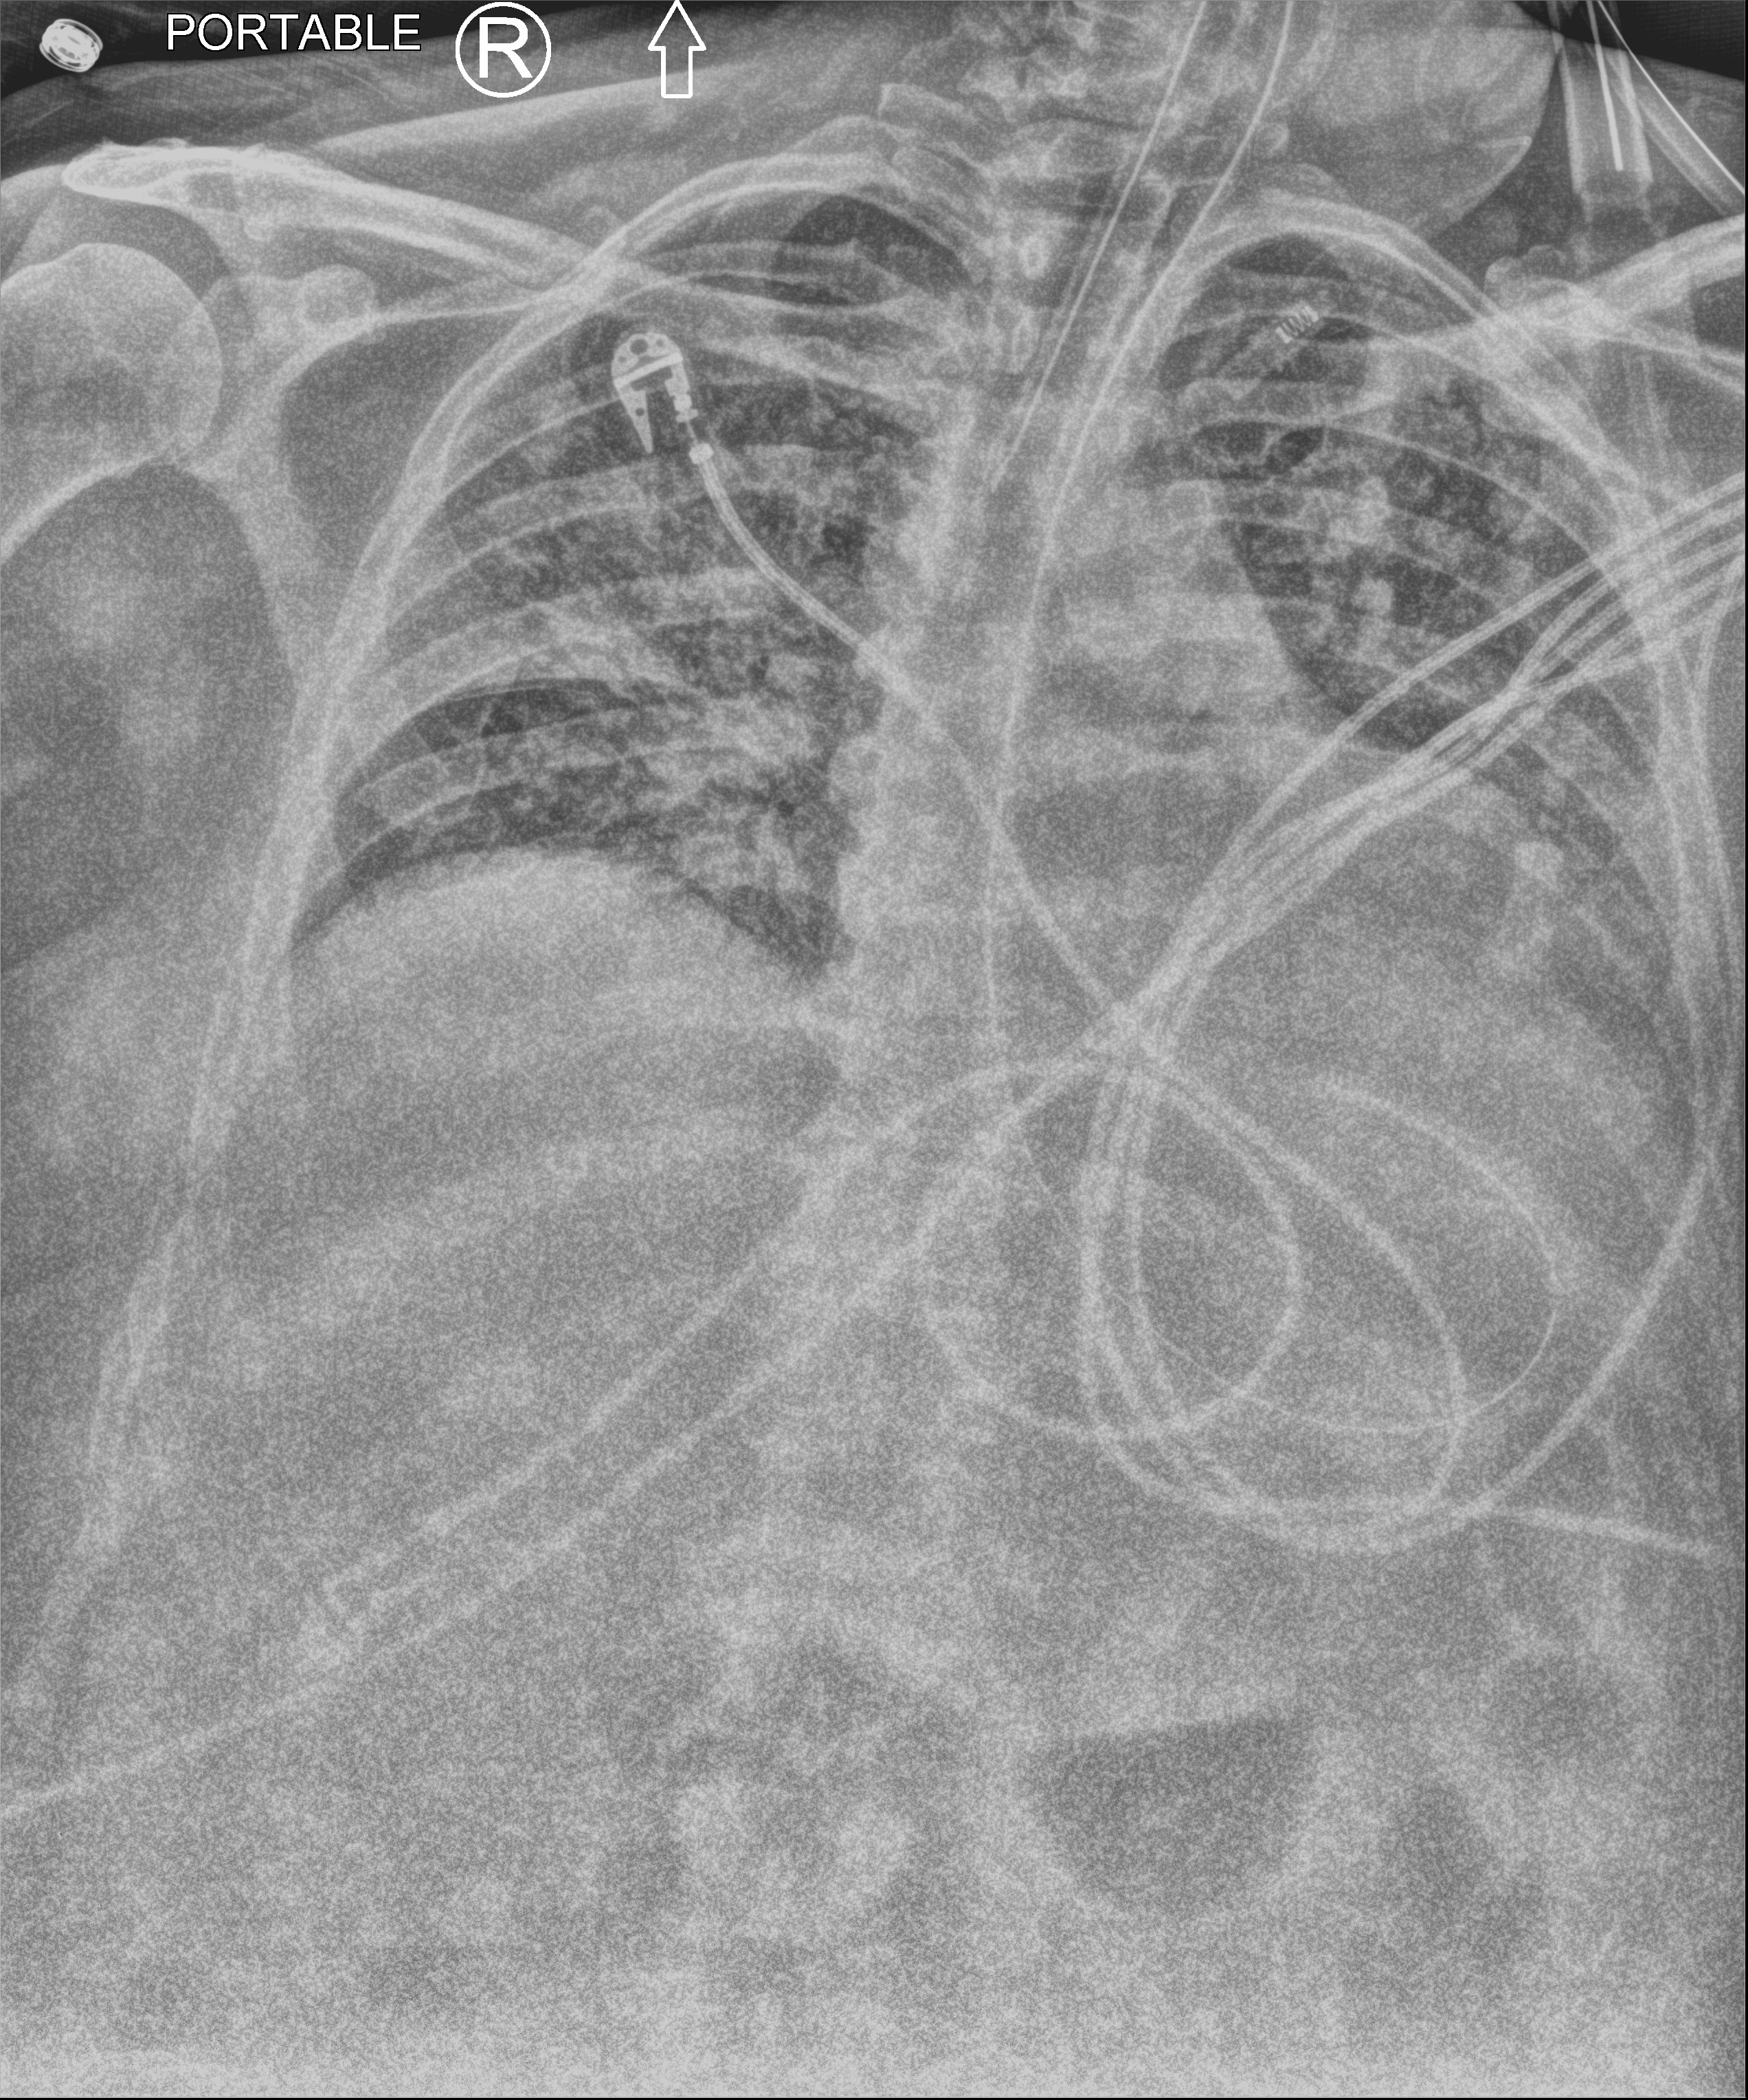
Bedside chest radiograph (computed radiography), anteroposterior (AP) projection. Patient hospitalised with COVID-19, aged 18–59 years.
Hospital-stay facts (about this admission, not read from this image; timing relative to this image not recorded):
- mechanically ventilated during this hospital stay: yes